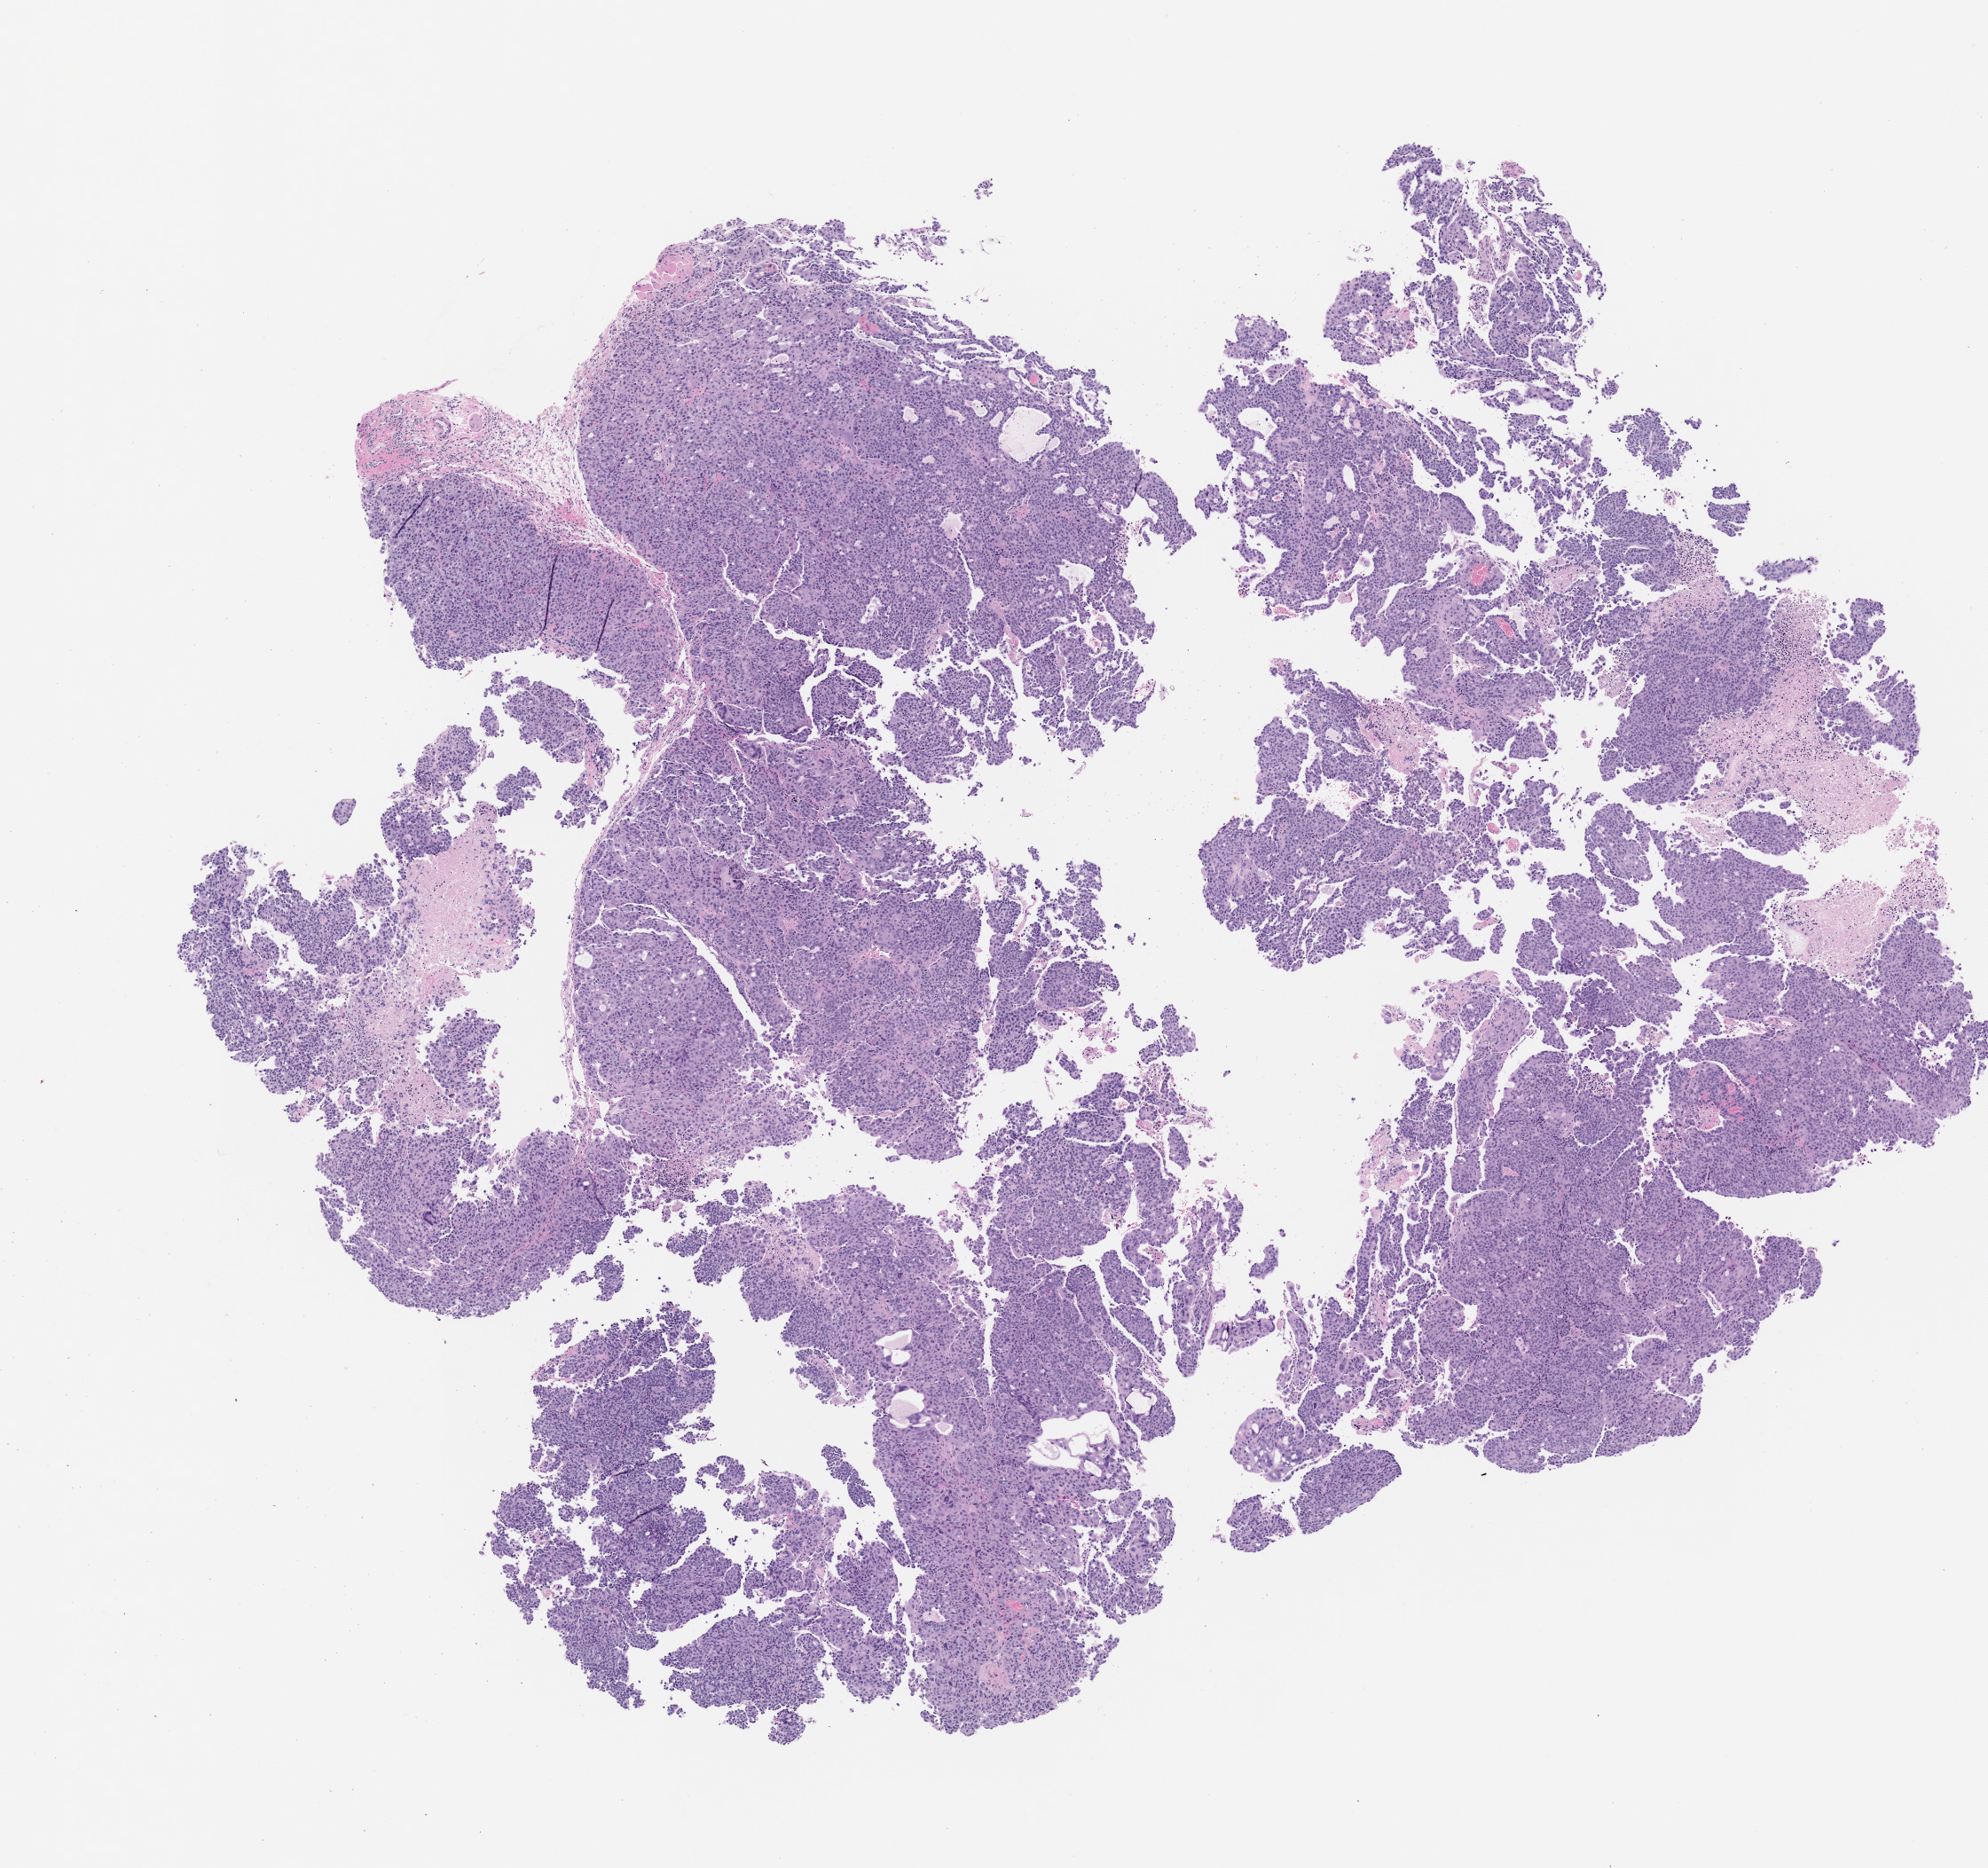
Whole-slide image, haematoxylin and eosin: patient-derived xenograft (human tumor grown in a mouse), passage 3, shown as a low-resolution overview of the whole scanned area (about 9.0 x 8.5 mm). Formalin-fixed paraffin-embedded section. Originating tumor site category: bladder.
Originating patient diagnosis: Urothelial Carcinoma.